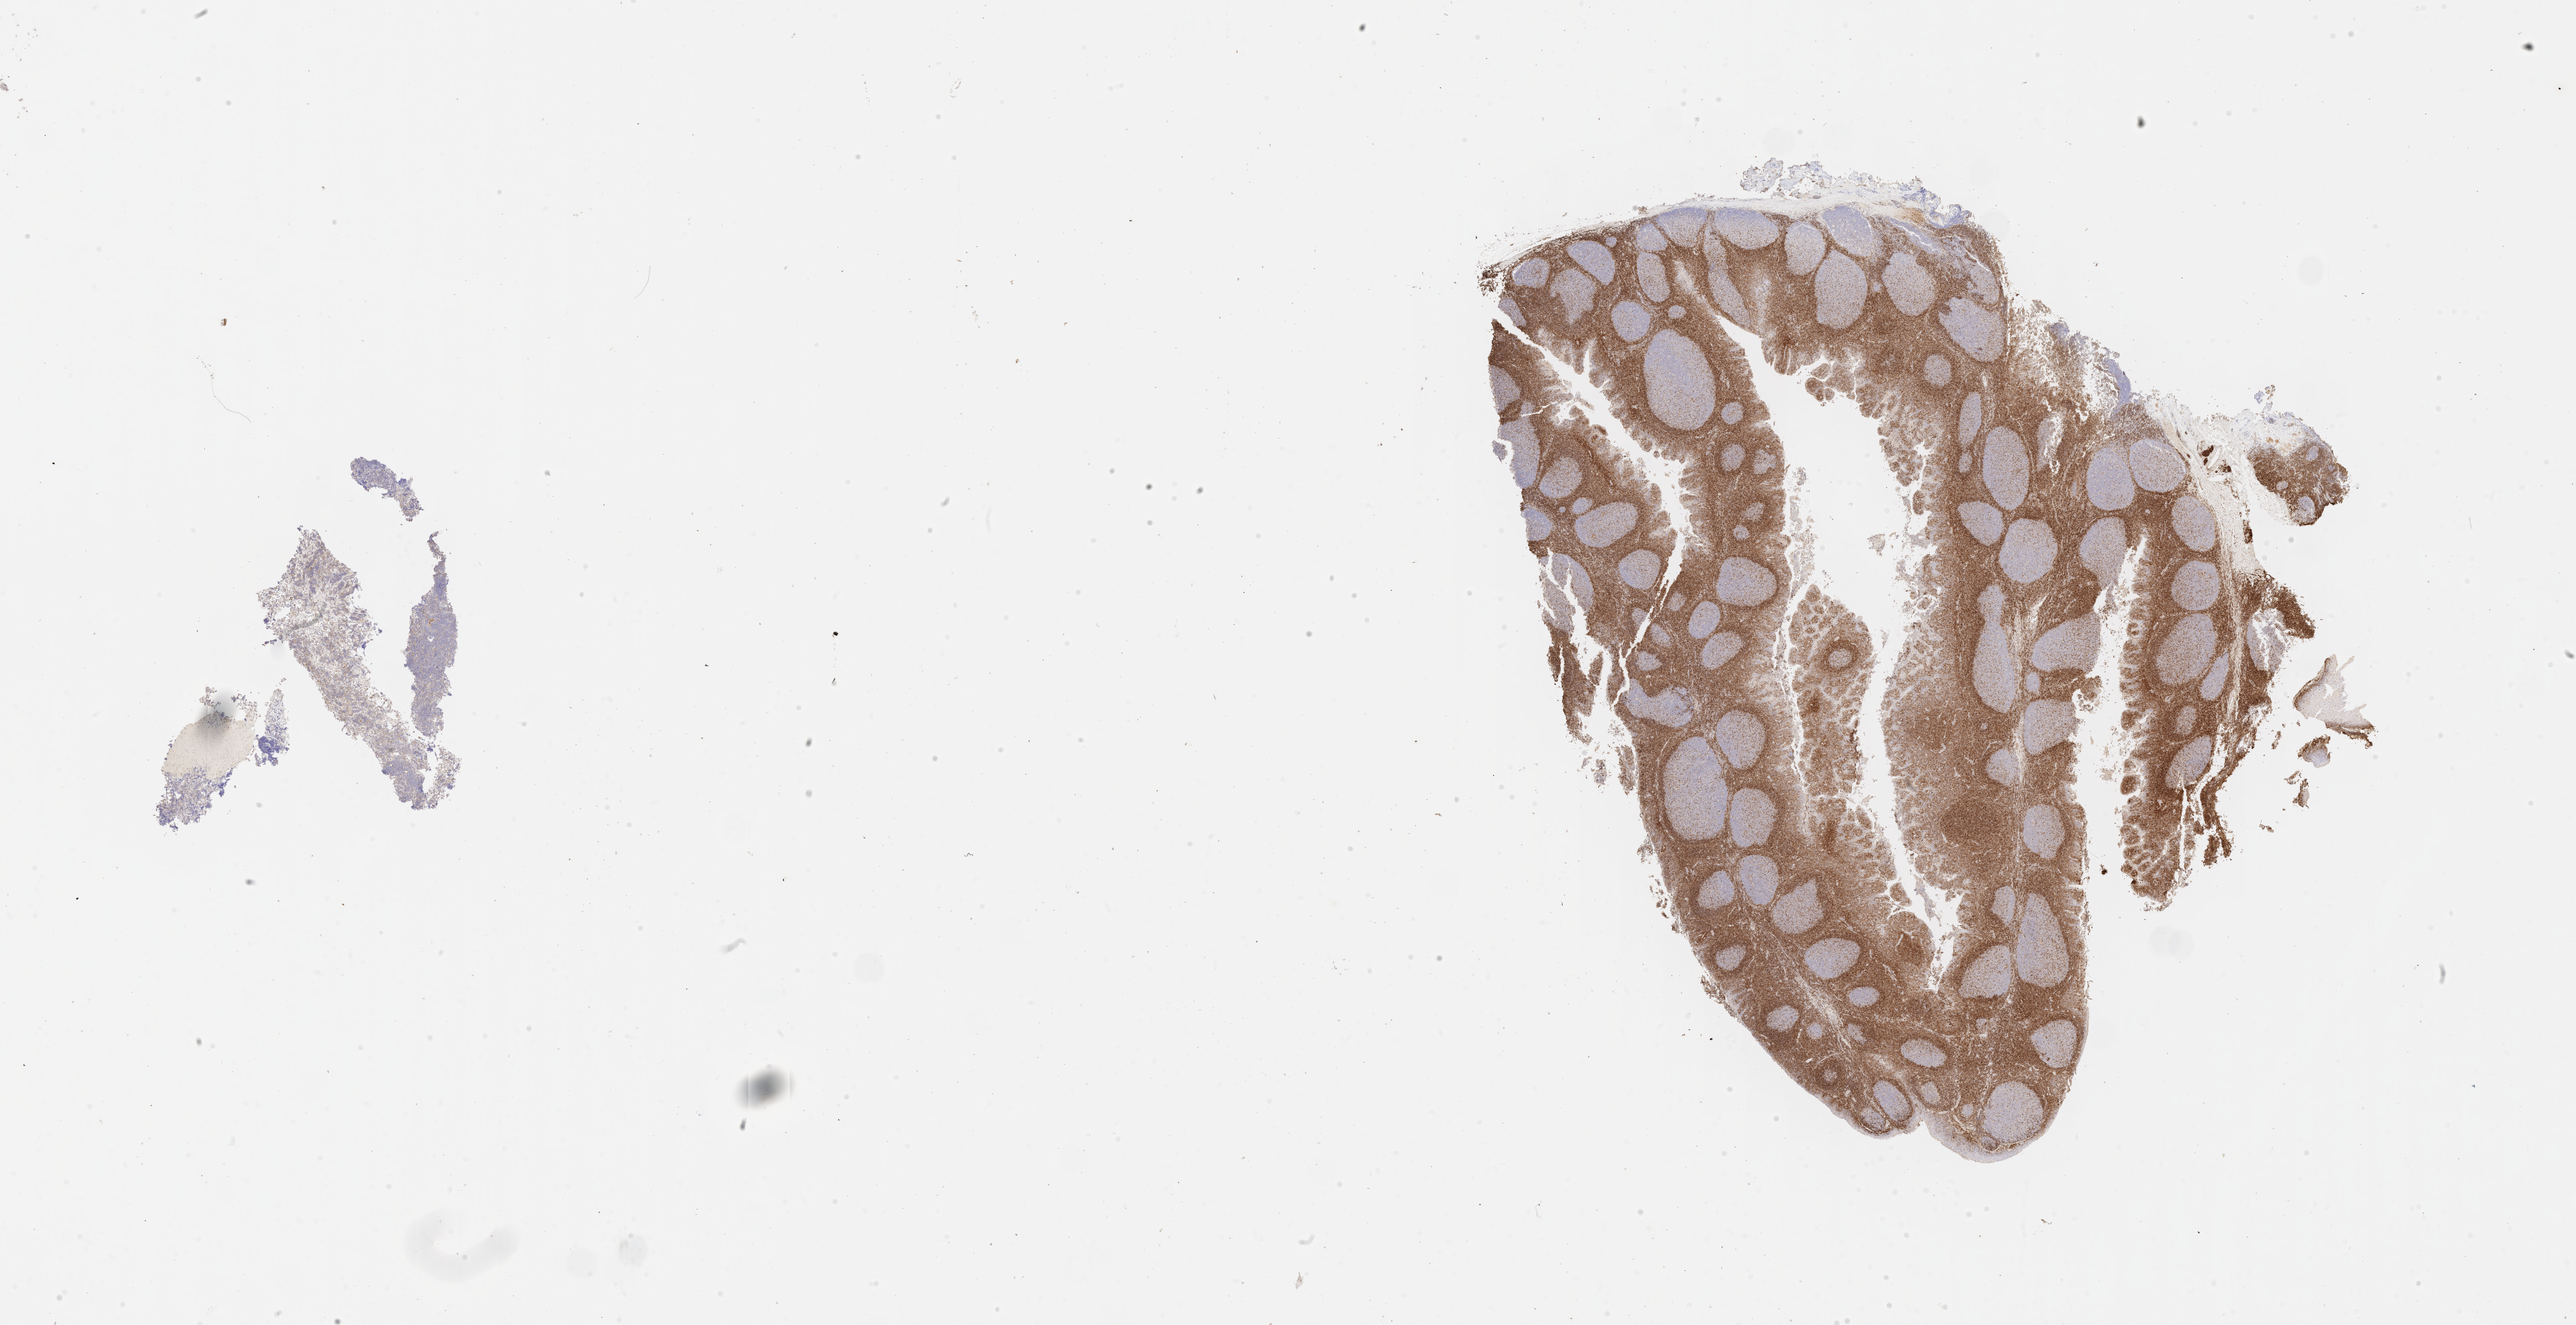
IHC for BCL2, whole-slide image, whole scanned area (about 31.2 x 16.0 mm) shown as a low-resolution overview. Specimen: tumor tissue. Anatomic site: pelvis. Female, age 7 years at initial diagnosis.
Histologic diagnosis: Burkitt lymphoma, NOS.